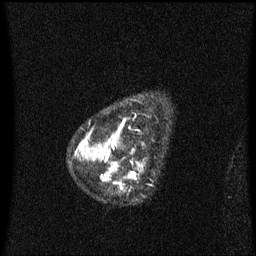
Breast MRI (dynamic contrast-enhanced), one sagittal slice. Slice 50 of 60 in the series (ordered by position). Dynamic contrast-enhanced series, image 2 of 3 at this slice position (ordered by acquisition). 1.5 T. TE 4.2 ms, TR 8.4 ms. 2 mm slice thickness. 256 × 256 image matrix, field of view 200 × 200 mm. Female patient, age 48 years. From the clinical record (not read from this slice): setting: breast cancer imaged before/during neoadjuvant chemotherapy; receptor status: HR-positive, HER2-negative.
Annotated regions visible in this slice (semi-automatic segmentation, software-assisted and operator-edited):
- analysis volume of interest (the breast-tissue region the enhancement analysis was run in; not a lesion): bounding box [x1, y1, x2, y2] px = [80, 126, 143, 192]
- tumour enhancement mask (voxels above the 70 % enhancement threshold inside the analysis volume of interest): [80, 134, 137, 190]